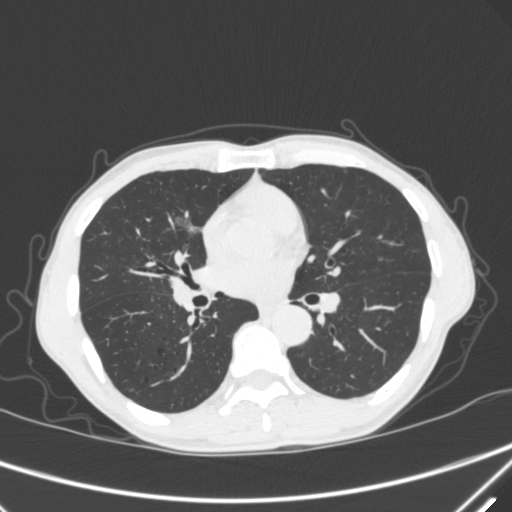
Chest CT, one axial slice; slice 173 of 340 in the series (ordered by position); 120 kVp; lung window (W 1500 / L -600 HU); 512 × 512 image matrix, field of view 350 × 350 mm. Patient: male, 67 years. Case-level facts recorded for this patient, not image findings: clinical TNM (as recorded): T1c N0 M0; histopathological grade: G1-2.
Outlined on this slice (rectangle marked by the reading radiologist):
- lung tumour (recorded histology: adenocarcinoma): bounding box <166,207,198,244> (left, top, right, bottom; pixels)